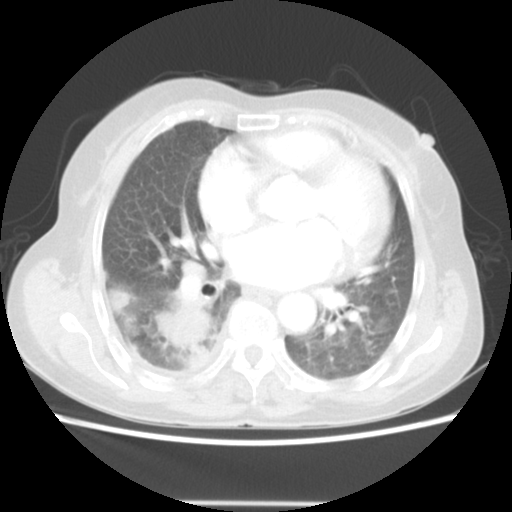
Chest CT, one axial slice; slice 24 of 52 in the series (ordered by position); reconstruction kernel STANDARD; 140 kVp; lung window (W 1500 / L -600 HU); 5 mm slice thickness; 512 × 512 image matrix. Female patient, age 67 years. Case-level facts recorded for this patient, not image findings: clinical TNM (as recorded): T3 N1 M1.
Outlined on this slice (bounding box drawn by a radiologist):
- lung tumour (recorded histology: adenocarcinoma): box from (x=154, y=294) to (x=214, y=363) px